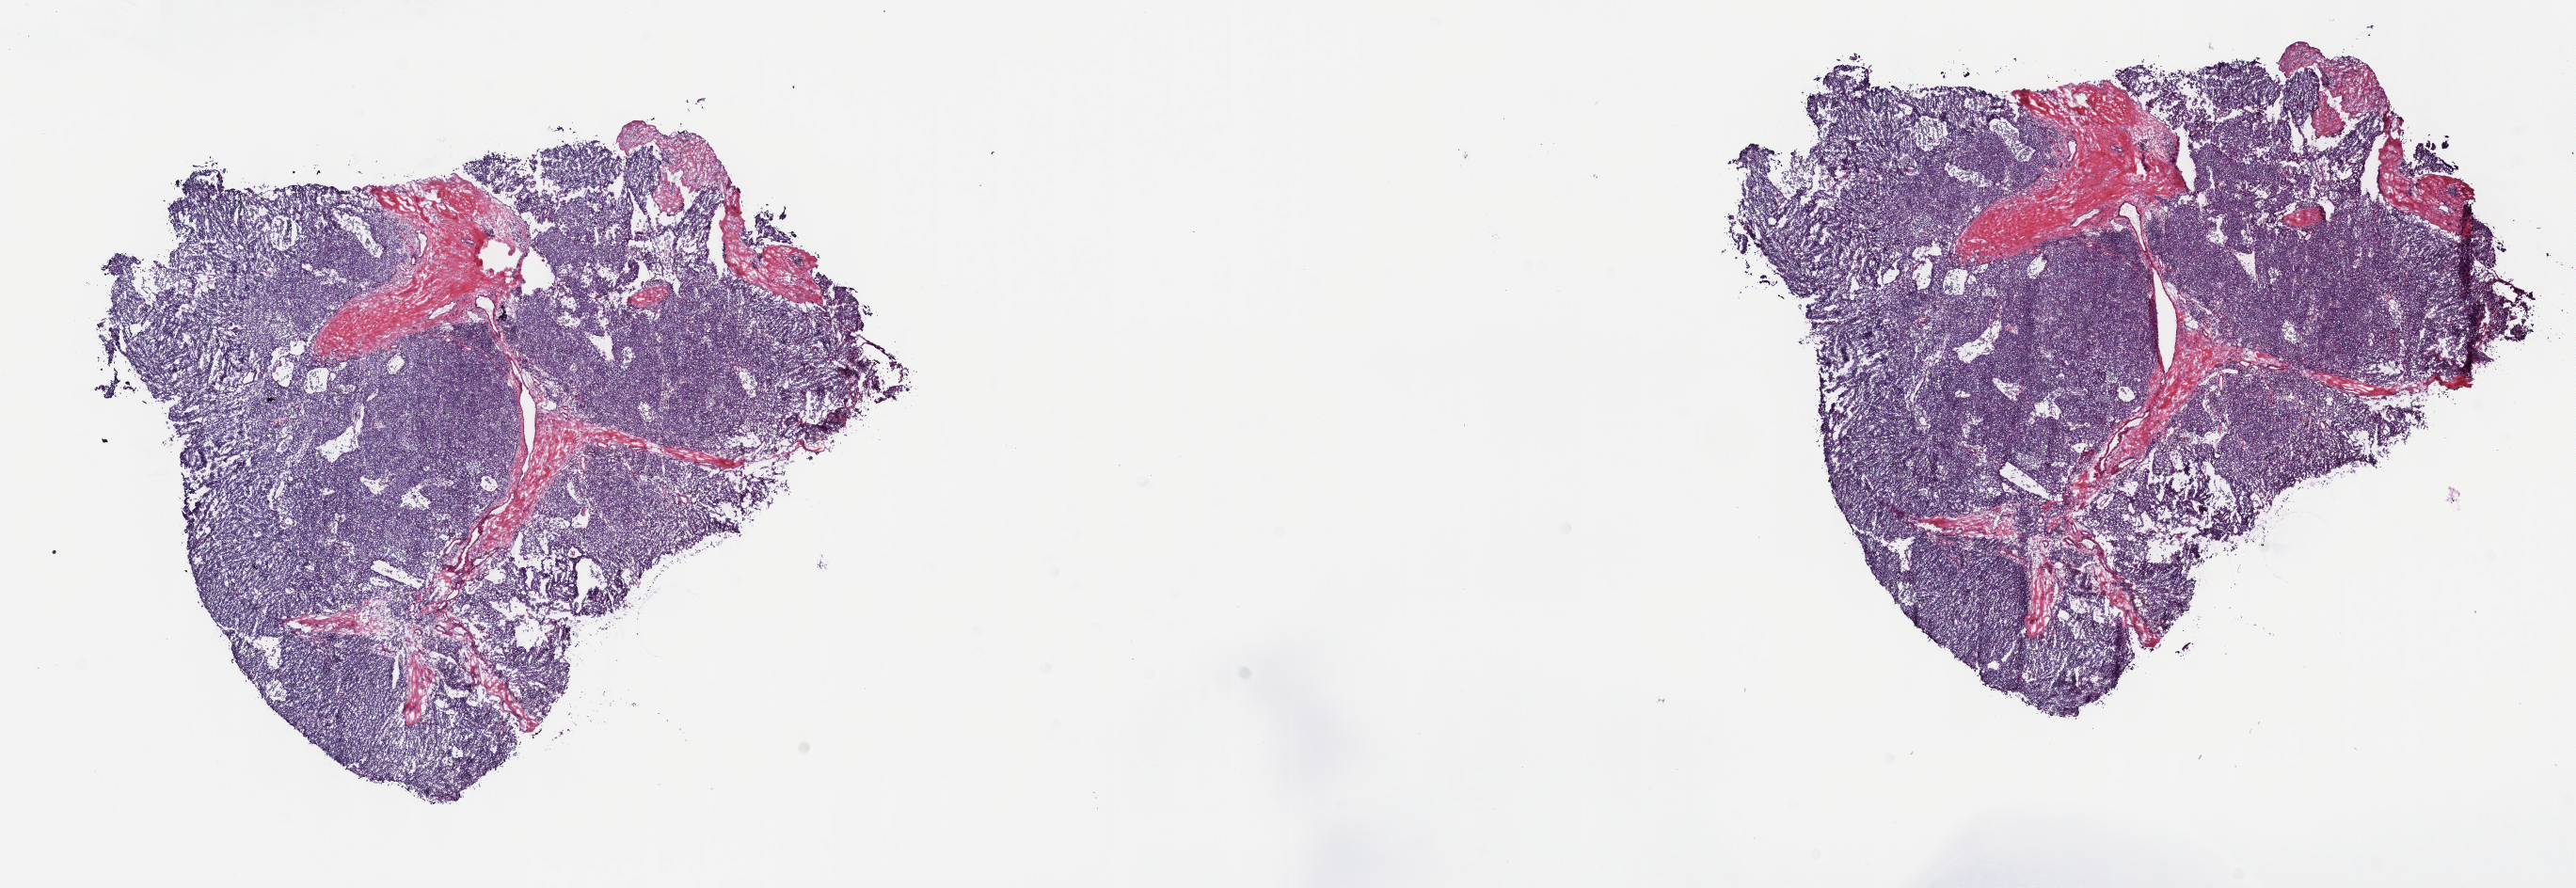
H&E-stained whole-slide image — whole scanned area (about 22.1 x 7.6 mm, slide scanned at 40x) shown as a low-resolution overview; frozen section from the top of the tissue portion; thymus, primary tumour sample. Male patient; age at initial diagnosis 39 years. Slide review estimates, as recorded: tumour cells 85%, tumour nuclei 98%, normal cells 0%, stromal cells 15%, necrosis 0%. Infiltration values recorded for this section: lymphocyte infiltration 0%, monocyte infiltration 0%, neutrophil infiltration 0%.
Diagnosis: Thymoma, type AB, malignant.